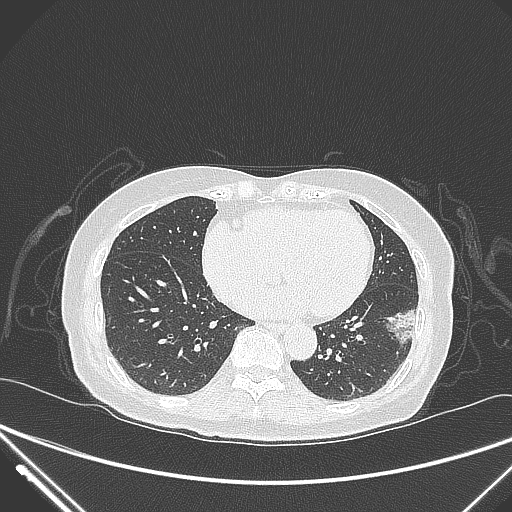
Chest CT, one axial slice. Slice 111 of 310 in the series (ordered by position). Lung window (W 1500 / L -600 HU). 1 mm slice thickness. 512 × 512 image matrix, field of view 377 × 377 mm. Female patient, age 82 years. Case-level facts recorded for this patient, not image findings: clinical TNM (as recorded): T1c N0 M0; histopathological grade: G2.
Outlined on this slice (bounding box drawn by a radiologist):
- lung tumour (recorded histology: adenocarcinoma): bounding box [x1, y1, x2, y2] px = [381, 300, 417, 353]